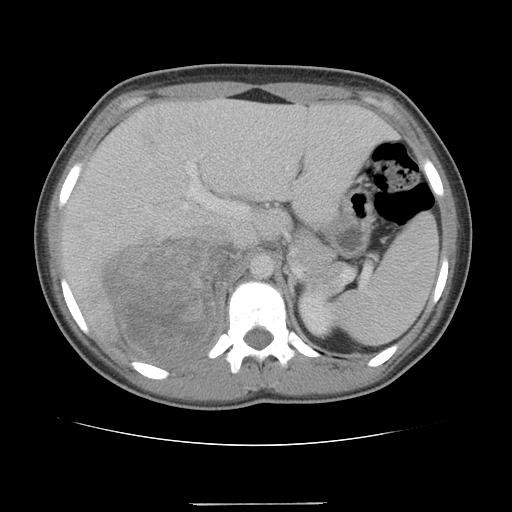
Contrast-enhanced abdominal CT, one axial slice; slice 75 of 100 in the series (ordered by position); reconstruction kernel STANDARD; intravenous contrast given; soft-tissue window (W 400 / L 40 HU); 5 mm slice thickness; 512 × 512 image matrix, field of view 360 × 360 mm. Female patient, age 21 years. From the clinical record (not read from this slice): diagnosis: adrenocortical carcinoma; tumour side: right adrenal; tumour size at pathology: 15.5 cm; Ki-67 index: 26 %; stage (as recorded): 3.
Structures marked on this image (semi-automatic segmentation, software-assisted and operator-edited):
- mass: bounding box [x1, y1, x2, y2] px = [104, 241, 238, 360]